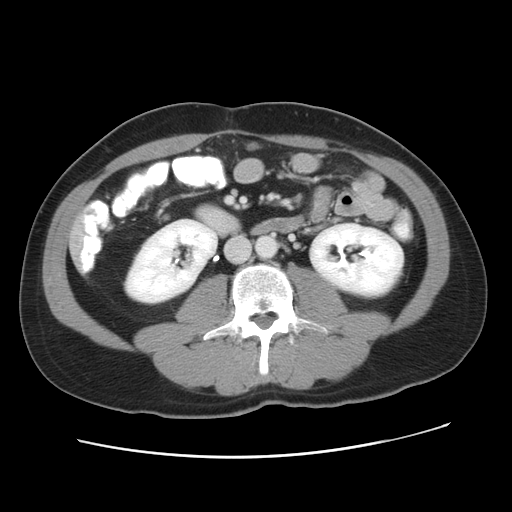
Contrast-enhanced abdominal CT, one axial slice; slice 13 of 49 in the series (ordered by position); reconstruction kernel STANDARD; 120 kVp; intravenous contrast given; soft-tissue window (W 400 / L 40 HU); 5 mm slice thickness; 512 × 512 image matrix, field of view 363 × 363 mm. Male patient, age 41 years. Case-level facts recorded for this patient, not image findings: diagnosis: colorectal cancer liver metastases, imaged before liver resection; multiple liver metastases: yes; largest metastasis: 0.7 cm.
Annotated regions visible in this slice (outlined manually by an expert reader):
- liver: bounding box (x1, y1, x2, y2) in pixels: (75, 240, 76, 247)